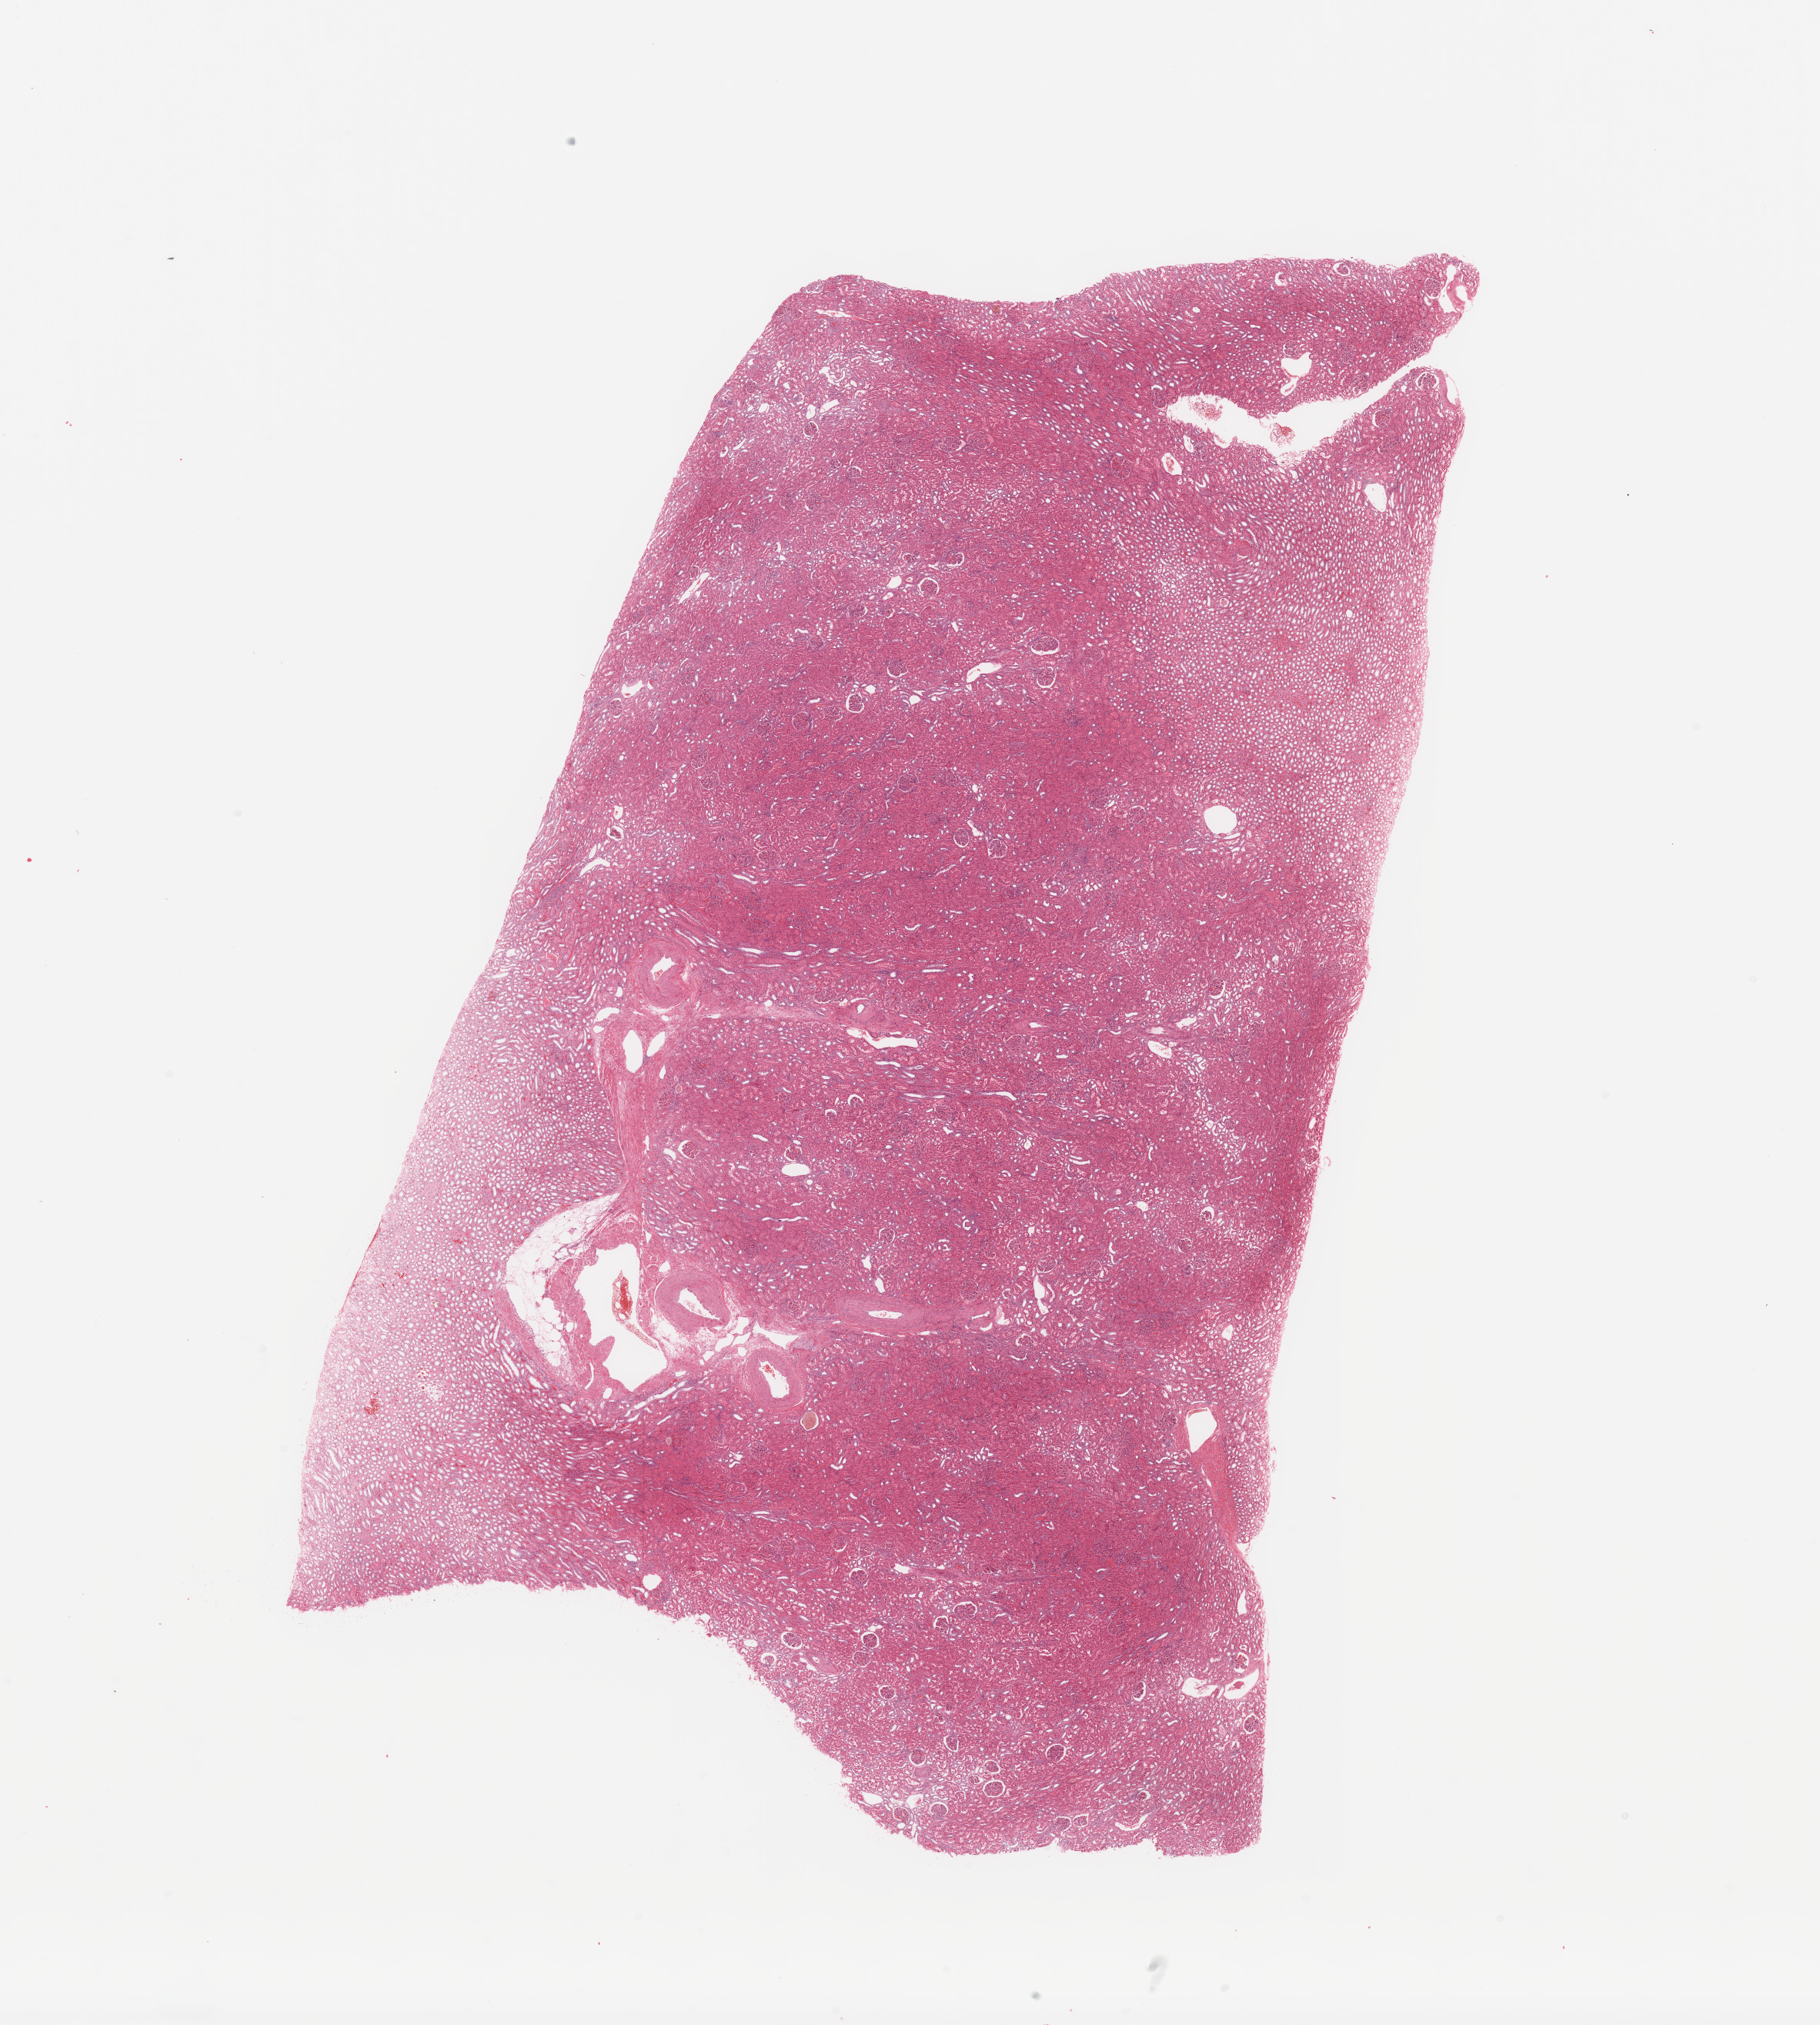
H&E-stained whole-slide image, shown as a low-resolution overview of the whole scanned area (about 18.7 x 20.8 mm, acquisition: 20x scan). Normal (non-tumour) tissue sample, sampled site: kidney. 52-year-old male patient.
* this section: normal (non-tumour) tissue from the same patient
* patient diagnosis: Renal cell carcinoma, NOS